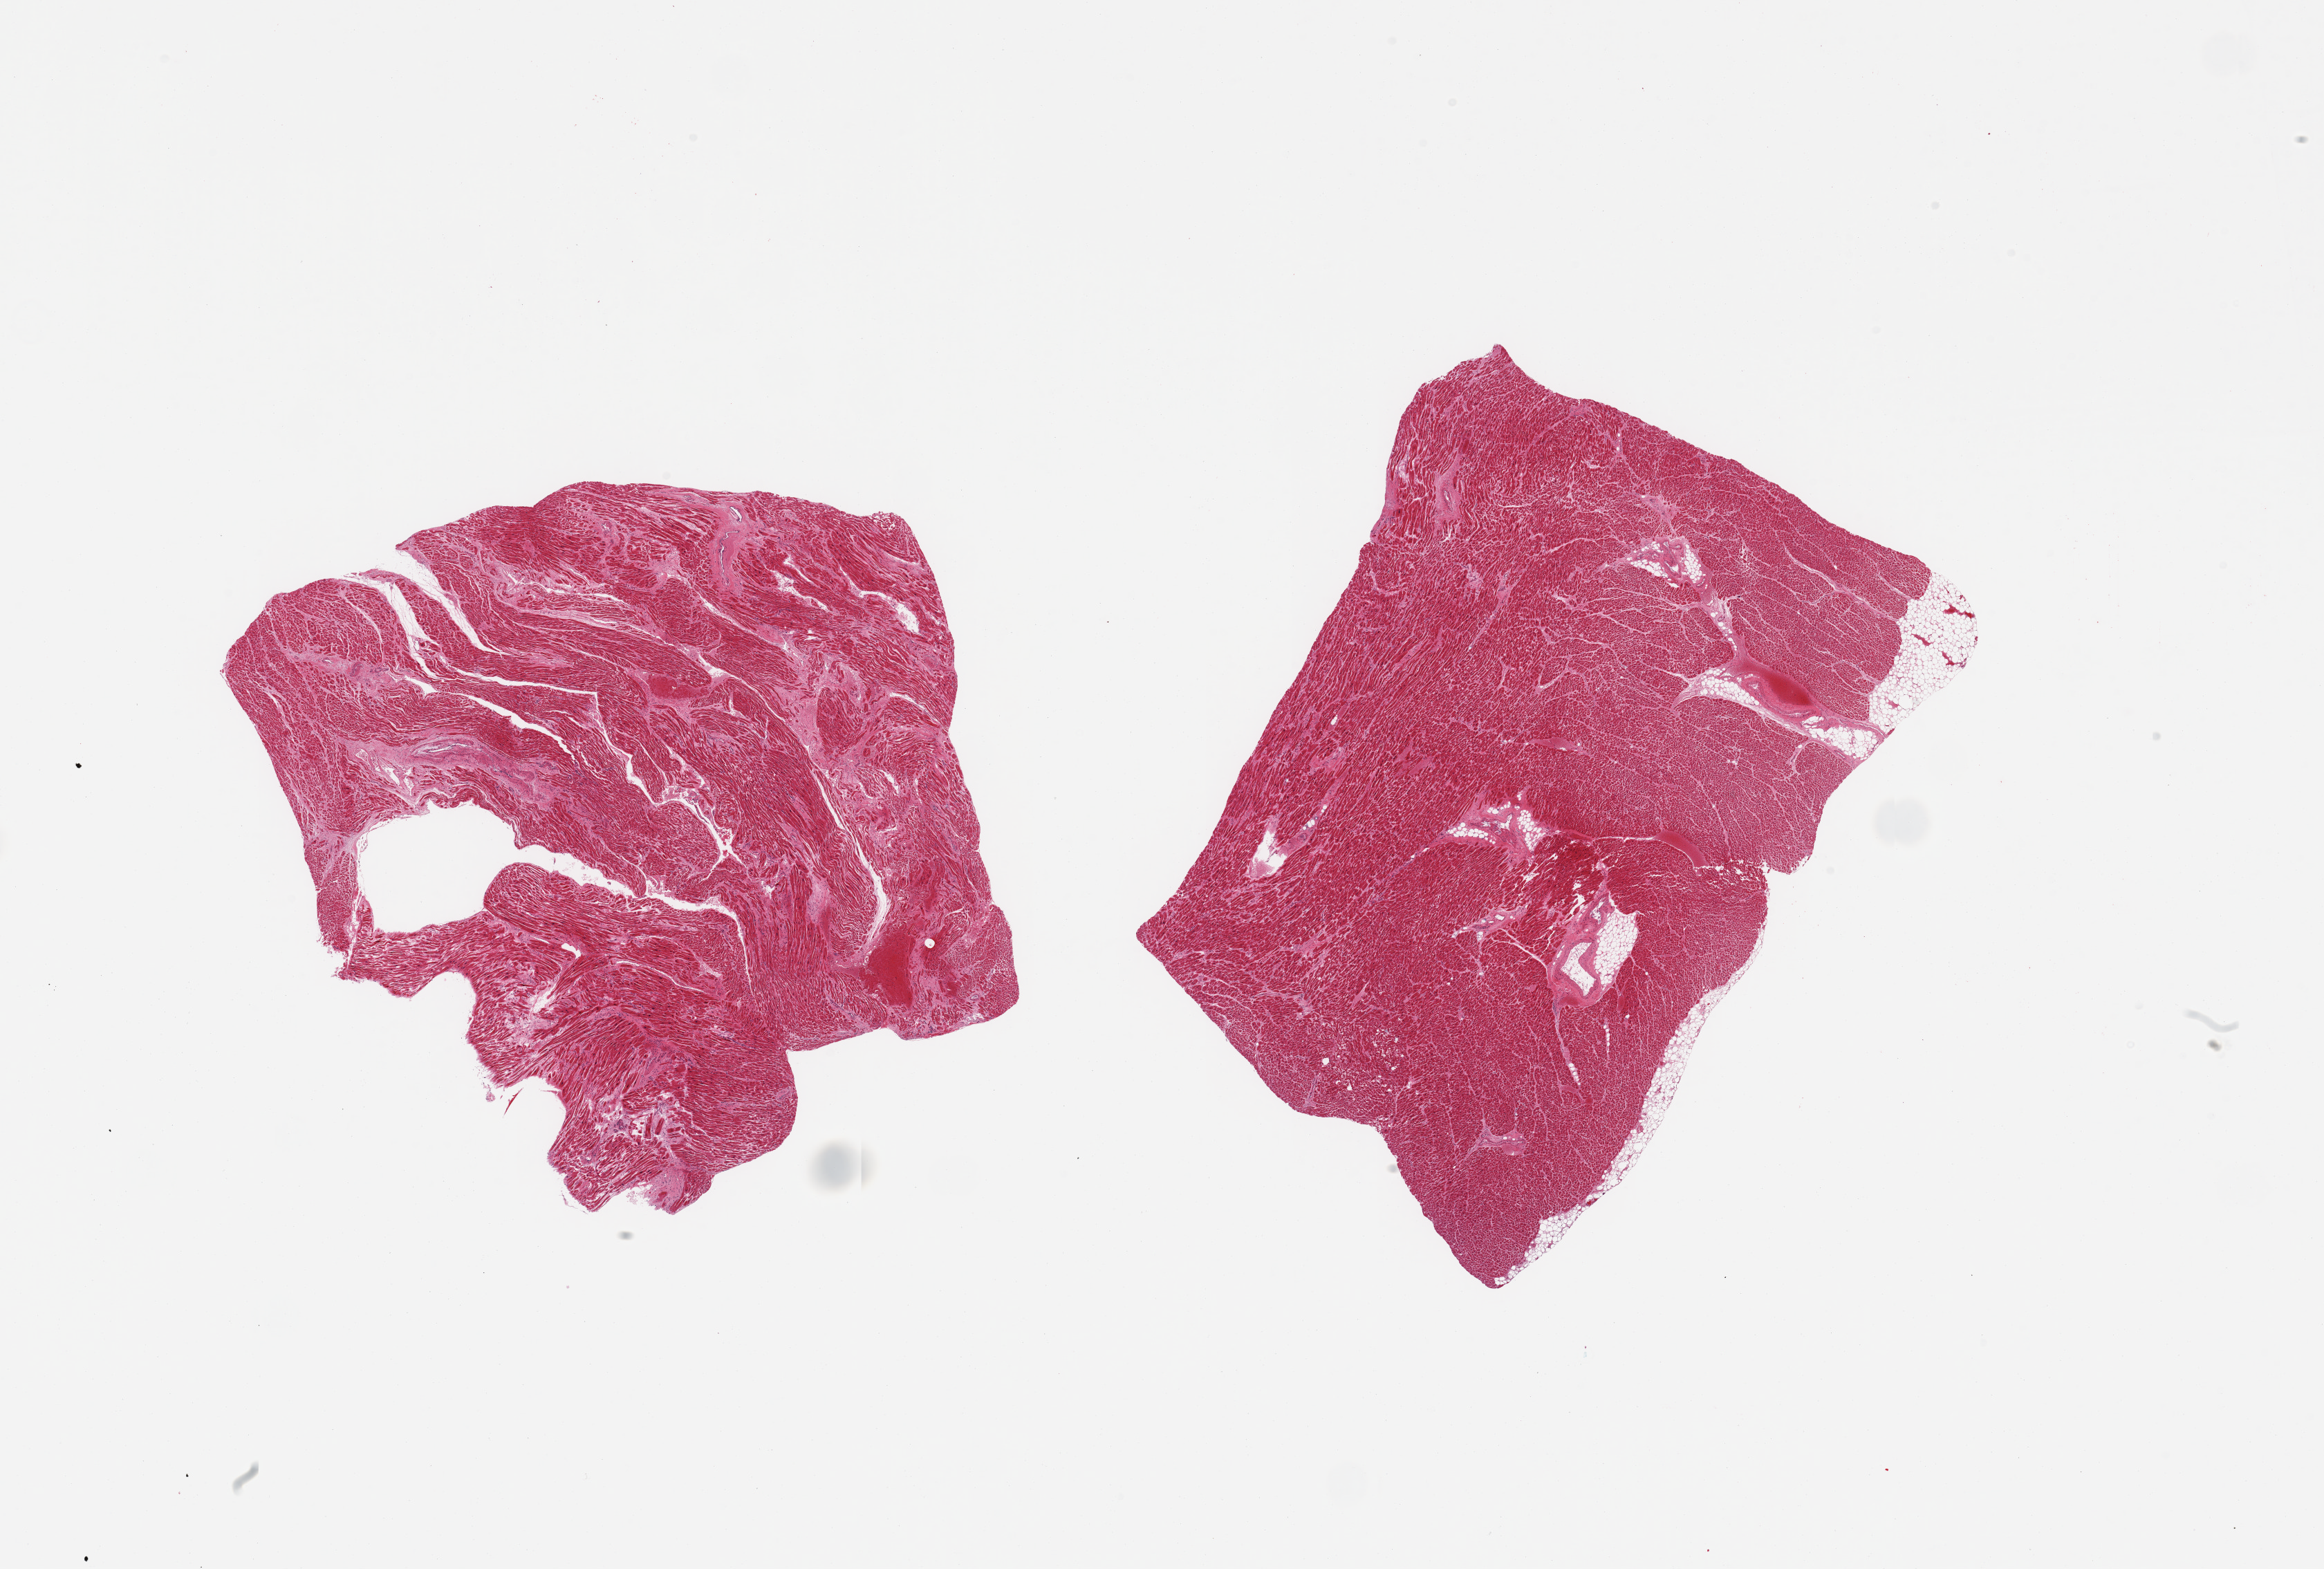
Digitized hematoxylin and eosin (H&E)-stained section, low-resolution overview of the scanned area, about 26.6 x 17.9 mm (acquisition: 20x scan). PAXgene-fixed paraffin-embedded (PFPE) section. Sampled site (target tissue): heart. Tissue donor sample.
Review note (as recorded): 2 pieces, chronic ischemic changes/interstitital fibrosis, moderate-marked.